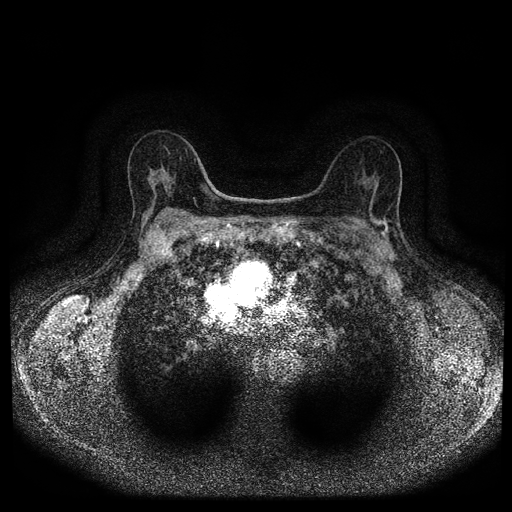
Breast MRI (dynamic contrast-enhanced, multi-phase), one axial slice; position 61 of 116 along the scan axis; dynamic contrast-enhanced series, time point 2 of 5 at this slice position (early post-contrast); 1.5 T; TE 2.7 ms, TR 5.4 ms; 2 mm slice thickness; 512 × 512 image matrix, field of view 330 × 330 mm. Patient: female, 63 years.
Annotated regions visible in this slice (semi-automatically segmented with operator editing):
- breast lesion (labelled 'tumour' in the annotation; benign lesions carry a separate 'benign' label): box from (x=373, y=217) to (x=392, y=239) px